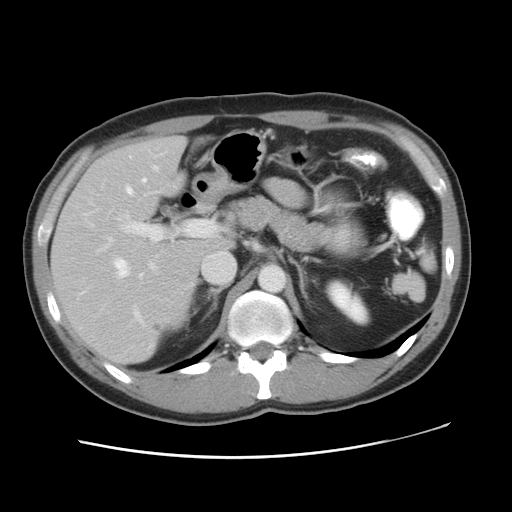
Contrast-enhanced abdominal CT, one axial slice. Slice 30 of 49 in the series (ordered by position). Reconstruction kernel STANDARD. Intravenous contrast given. Soft-tissue window (W 400 / L 40 HU). 5 mm slice thickness. 512 × 512 image matrix, field of view 363 × 363 mm. Male patient, age 41 years. From the clinical record (not read from this slice): diagnosis: colorectal cancer liver metastases, imaged before liver resection.
Annotated regions visible in this slice (expert manual segmentation):
- hepatic veins: bounding box <92,157,234,282> (left, top, right, bottom; pixels)
- liver: <53,138,229,364>
- planned liver remnant (the part of the liver to remain after resection): <103,138,230,249>
- portal vein (with intrahepatic branches): <90,202,212,322>
- liver metastasis: <155,323,161,333>
- liver metastasis: <154,324,162,333>